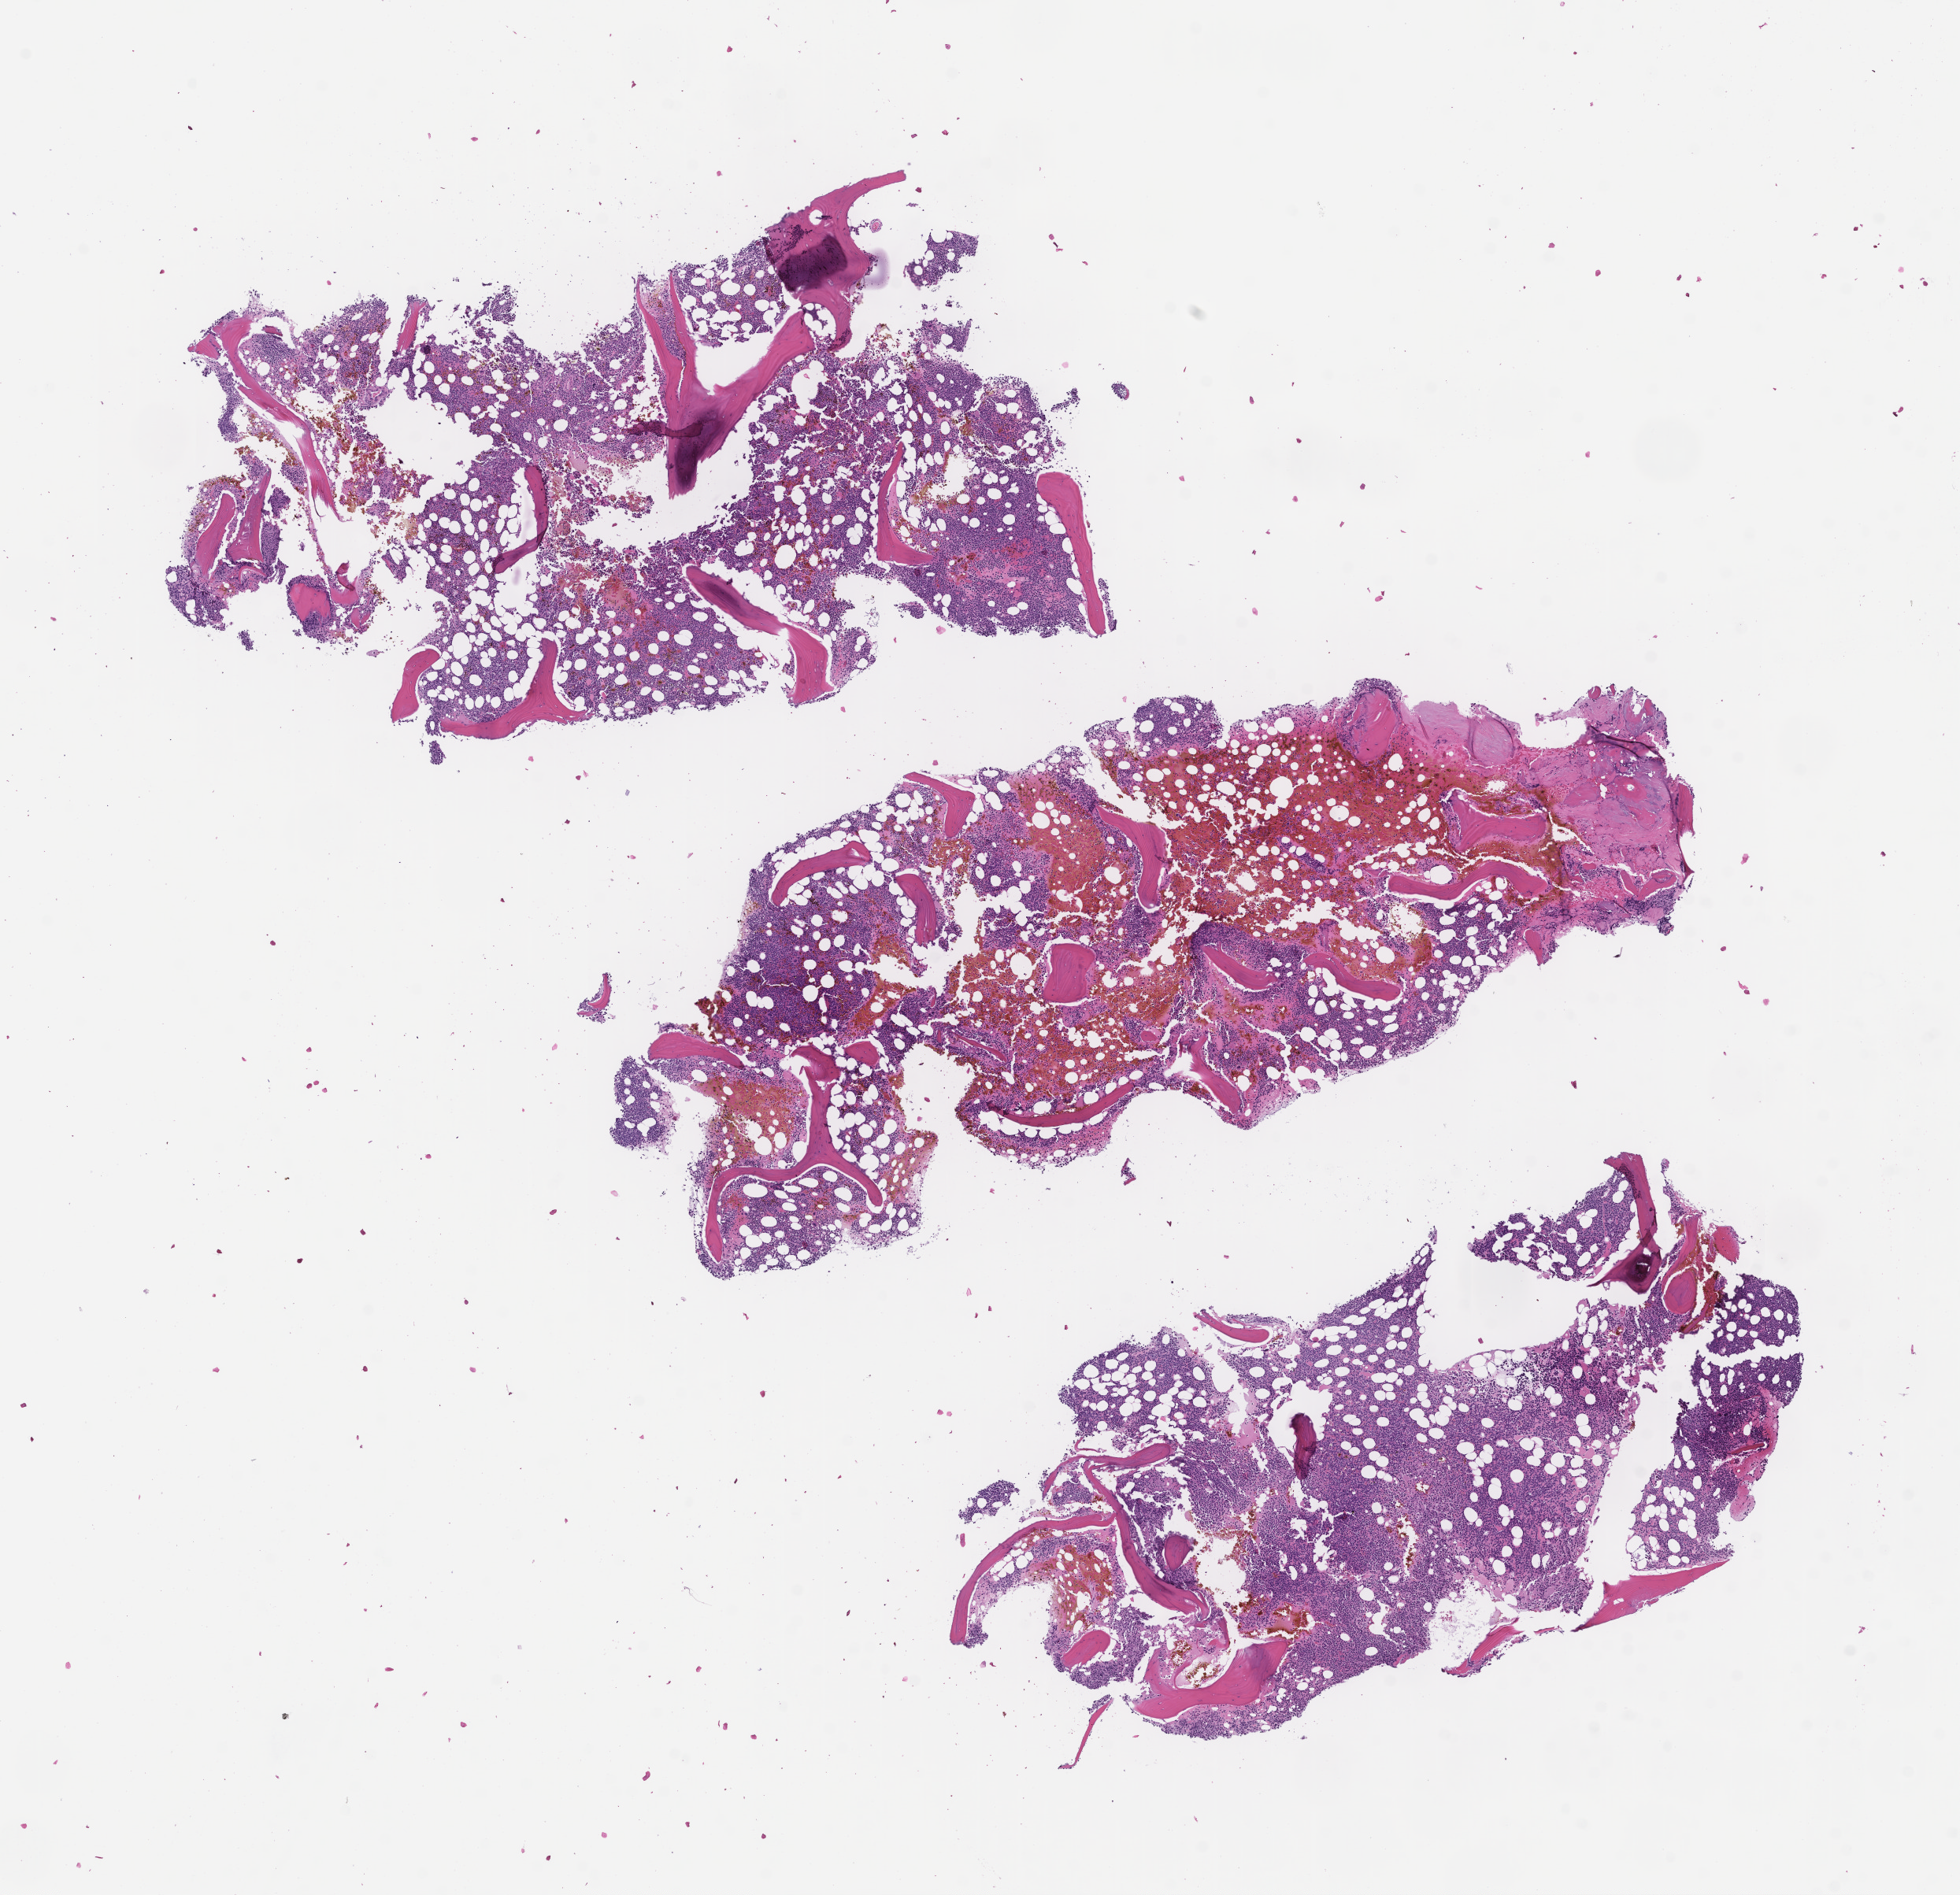
H&E whole-slide image — a low-resolution overview of the entire scanned area, about 10.1 x 9.7 mm; formalin-fixed, paraffin-embedded (FFPE) tissue; site: bone marrow. Patient: female.
This section: primary tumour tissue. Diagnosis: Plasma Cell Myeloma.